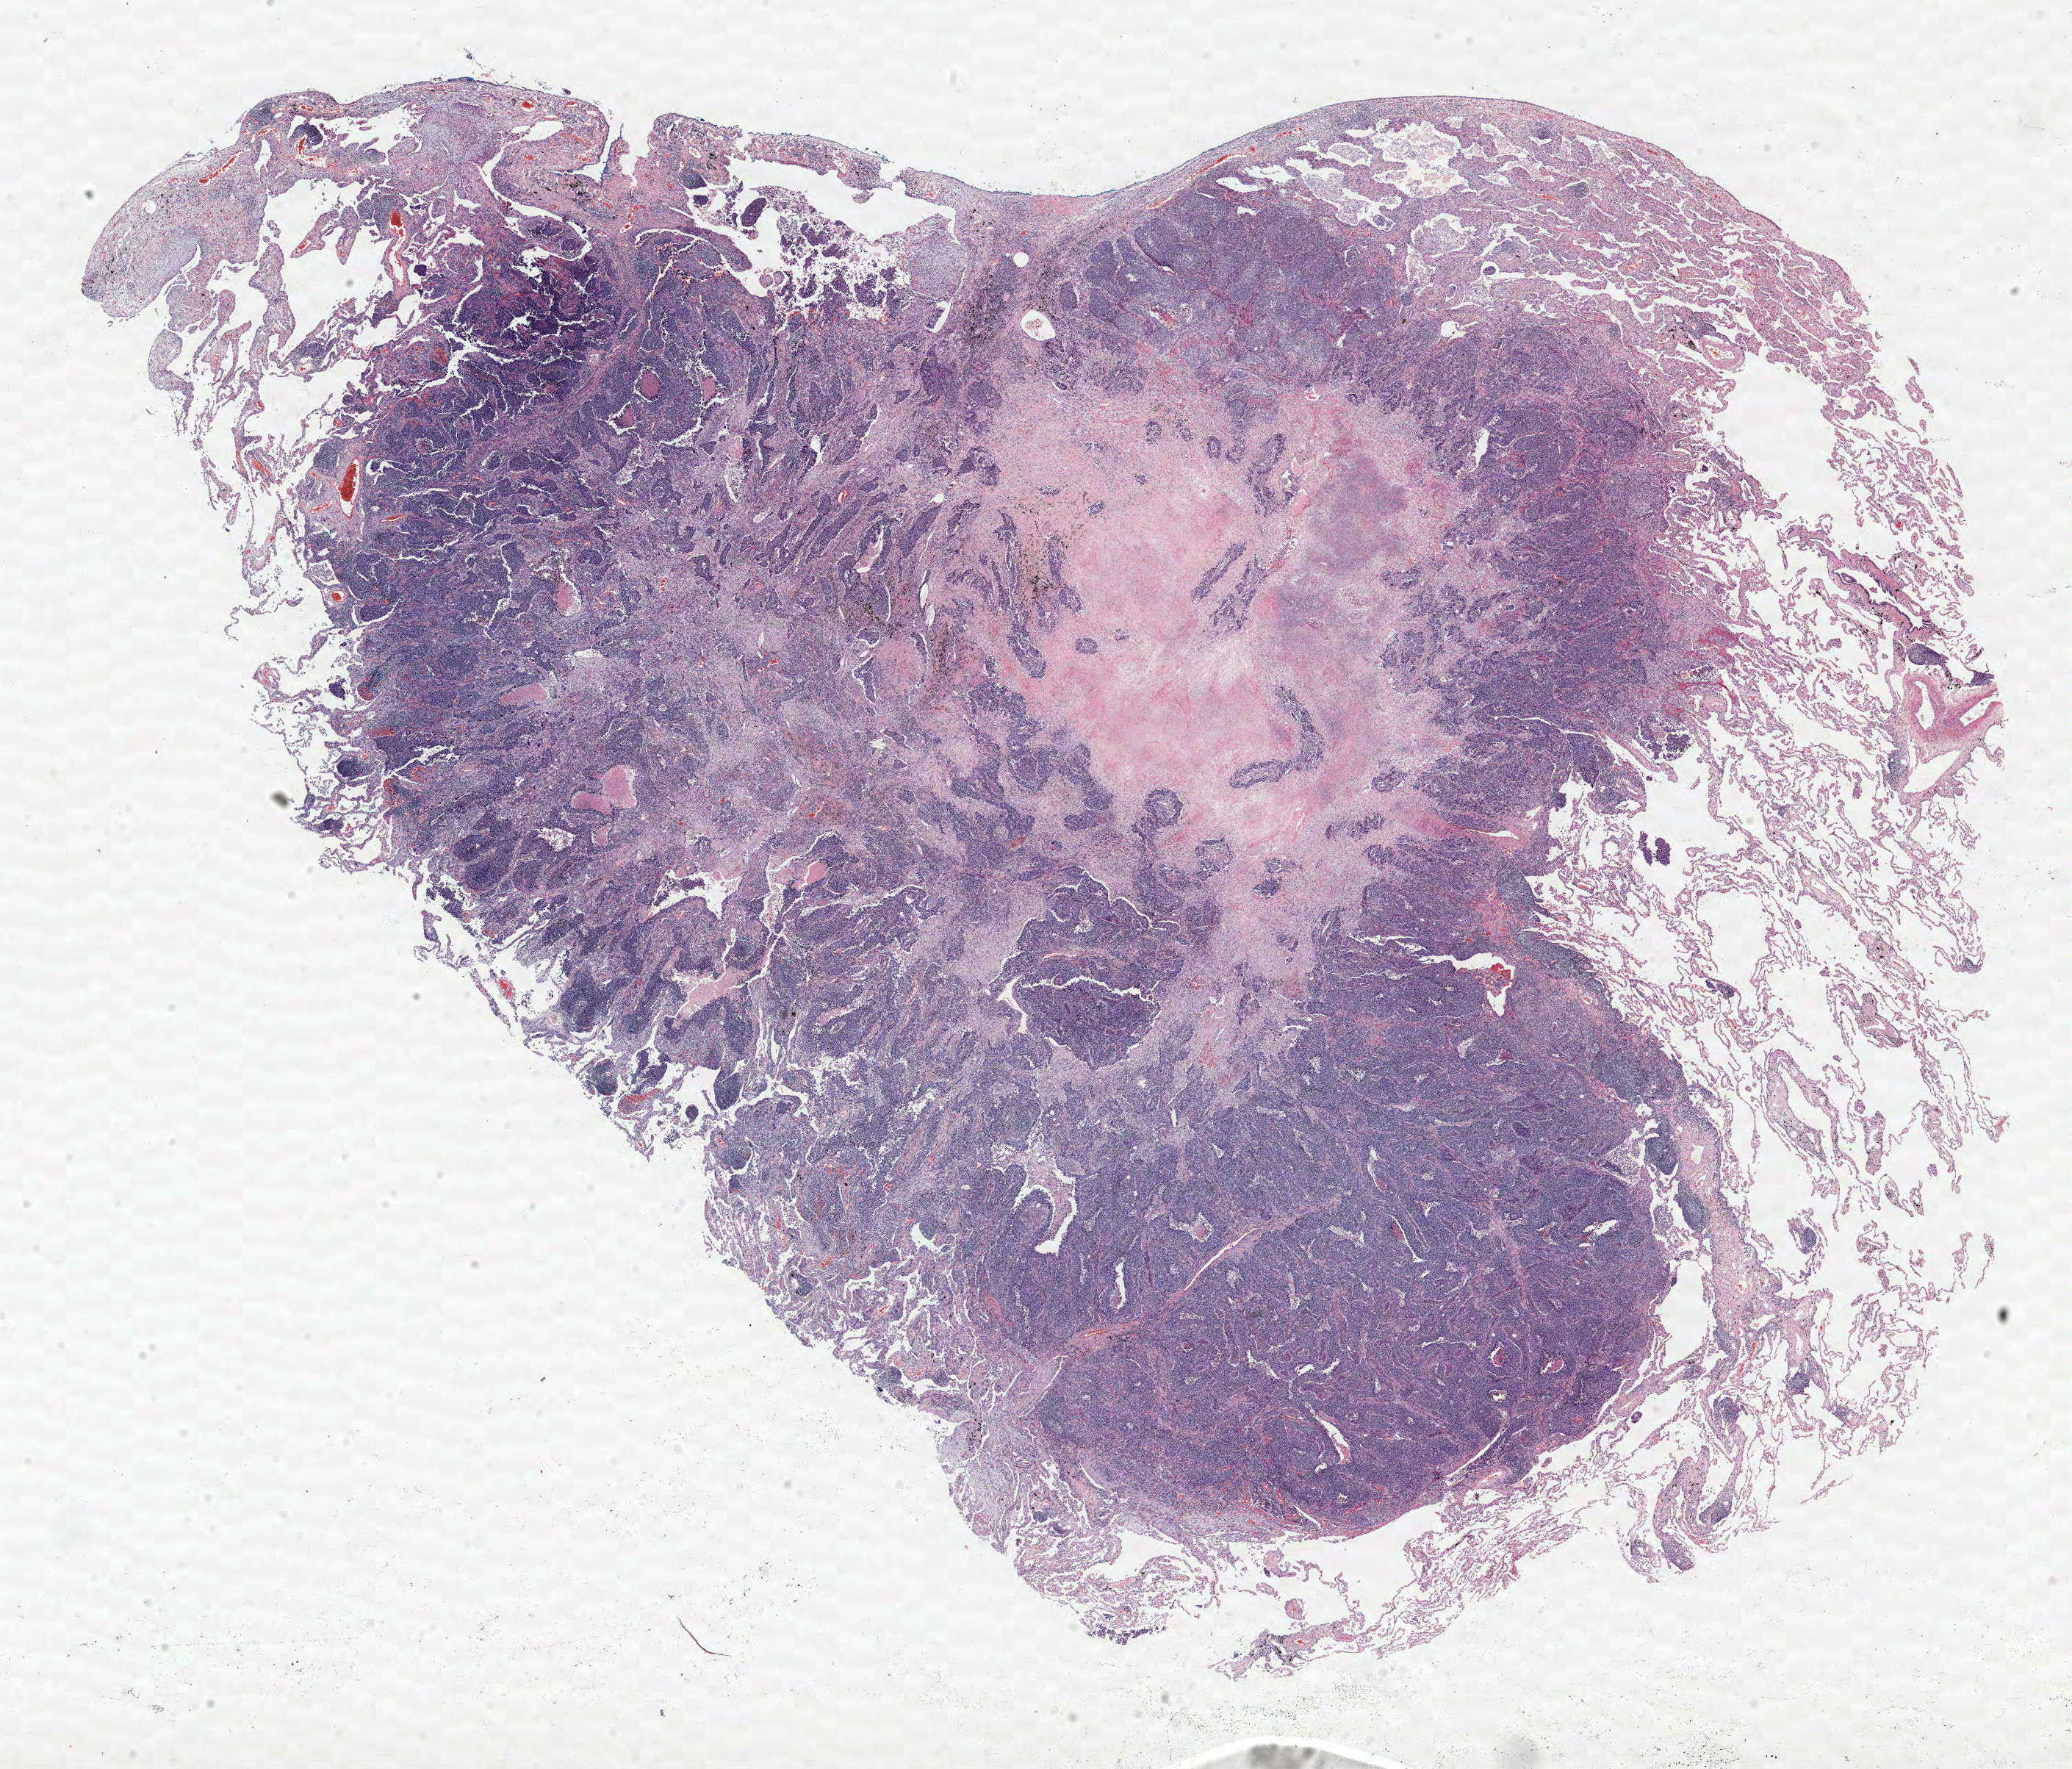
Hematoxylin and eosin (H&E) stained whole-slide image — a low-resolution overview of the entire scanned area, about 22.6 x 19.3 mm; FFPE section; lung. Male patient, aged 73 at enrolment. Former smoker at enrolment.
Participant's lung-cancer diagnosis: Adenocarcinoma, NOS (ICD-O-3 8140/3). Note: participant had 2 primary lung cancers recorded; fields above describe the first.